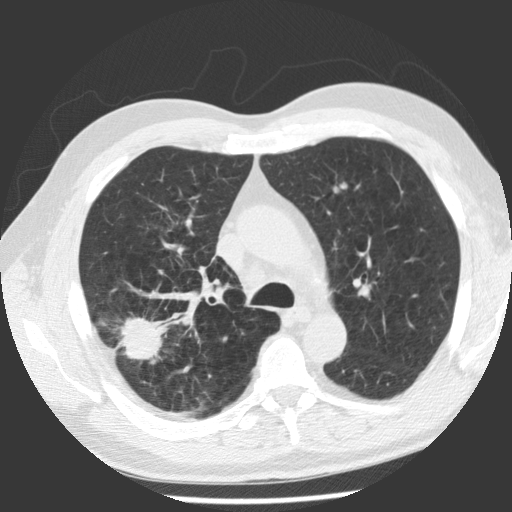
Low-dose screening chest CT, axial slice, baseline screening round, lung window (W 1500 / L -600 HU), 2.5 mm slice thickness, standard (soft-tissue) reconstruction kernel (STANDARD), 140 kVp, slice 76 of 112 in the series. Male participant, aged 62 years at enrolment. Former smoker at enrolment.
Expert reader's lesion annotation, bounding box [x1, y1, x2, y2] px = [107, 299, 181, 370]. The screening reader recorded 2 non-calcified nodules or masses ≥4 mm on this exam (right upper lobe, right upper lobe); which of them this box marks is not recorded. Official screen result: positive, change unspecified: nodule(s) >= 4 mm or enlarging nodule(s), mass(es), or other non-specific abnormalities suspicious for lung cancer. Later outcome: lung cancer diagnosed 71 days after this screen — adenocarcinoma, NOS, right upper lobe, poorly differentiated (G3), stage IV (AJCC 6th edition), 30 mm at pathology.